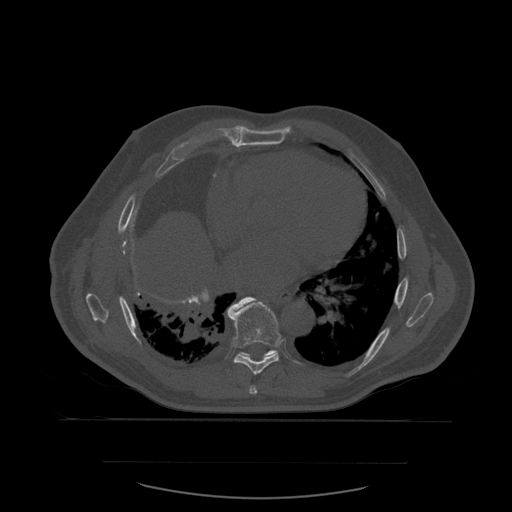
CT including the spine, one axial slice. Slice 358 of 590 in the series (ordered by position). Bone window (W 1800 / L 400 HU). 1.25 mm slice thickness. 512 × 512 image matrix, field of view 479 × 479 mm. Patient age 71 years. From the clinical record (not read from this slice): primary cancer: lung.
Annotated regions visible in this slice (semi-automatic segmentation, software-assisted and operator-edited):
- T7 vertebra: bounding box (x1, y1, x2, y2) in pixels: (250, 385, 258, 394)
- T8 vertebra: (227, 297, 282, 375)
- T9 vertebra: (248, 350, 275, 357)